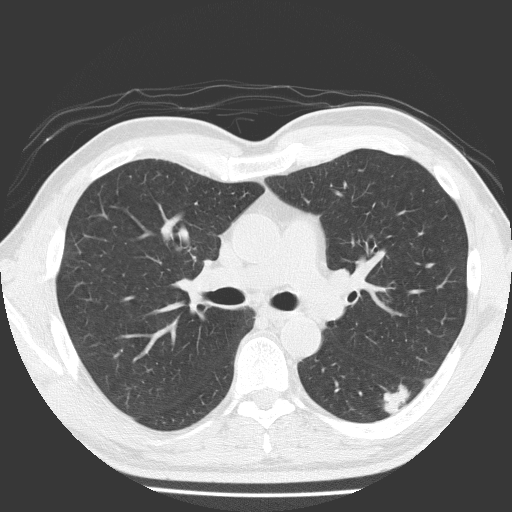
Low-dose screening chest CT, one axial slice. Position 112 of 184 along the scan axis. Reconstruction kernel FC51. 120 kVp. Lung window (W 1500 / L -600 HU). 512 × 512 image matrix, field of view 348 × 348 mm.
Outlined on this slice (expert manual segmentation):
- lesion 1 (tumor, lower lobe of left lung): bounding box [x1, y1, x2, y2] px = [383, 383, 410, 417]